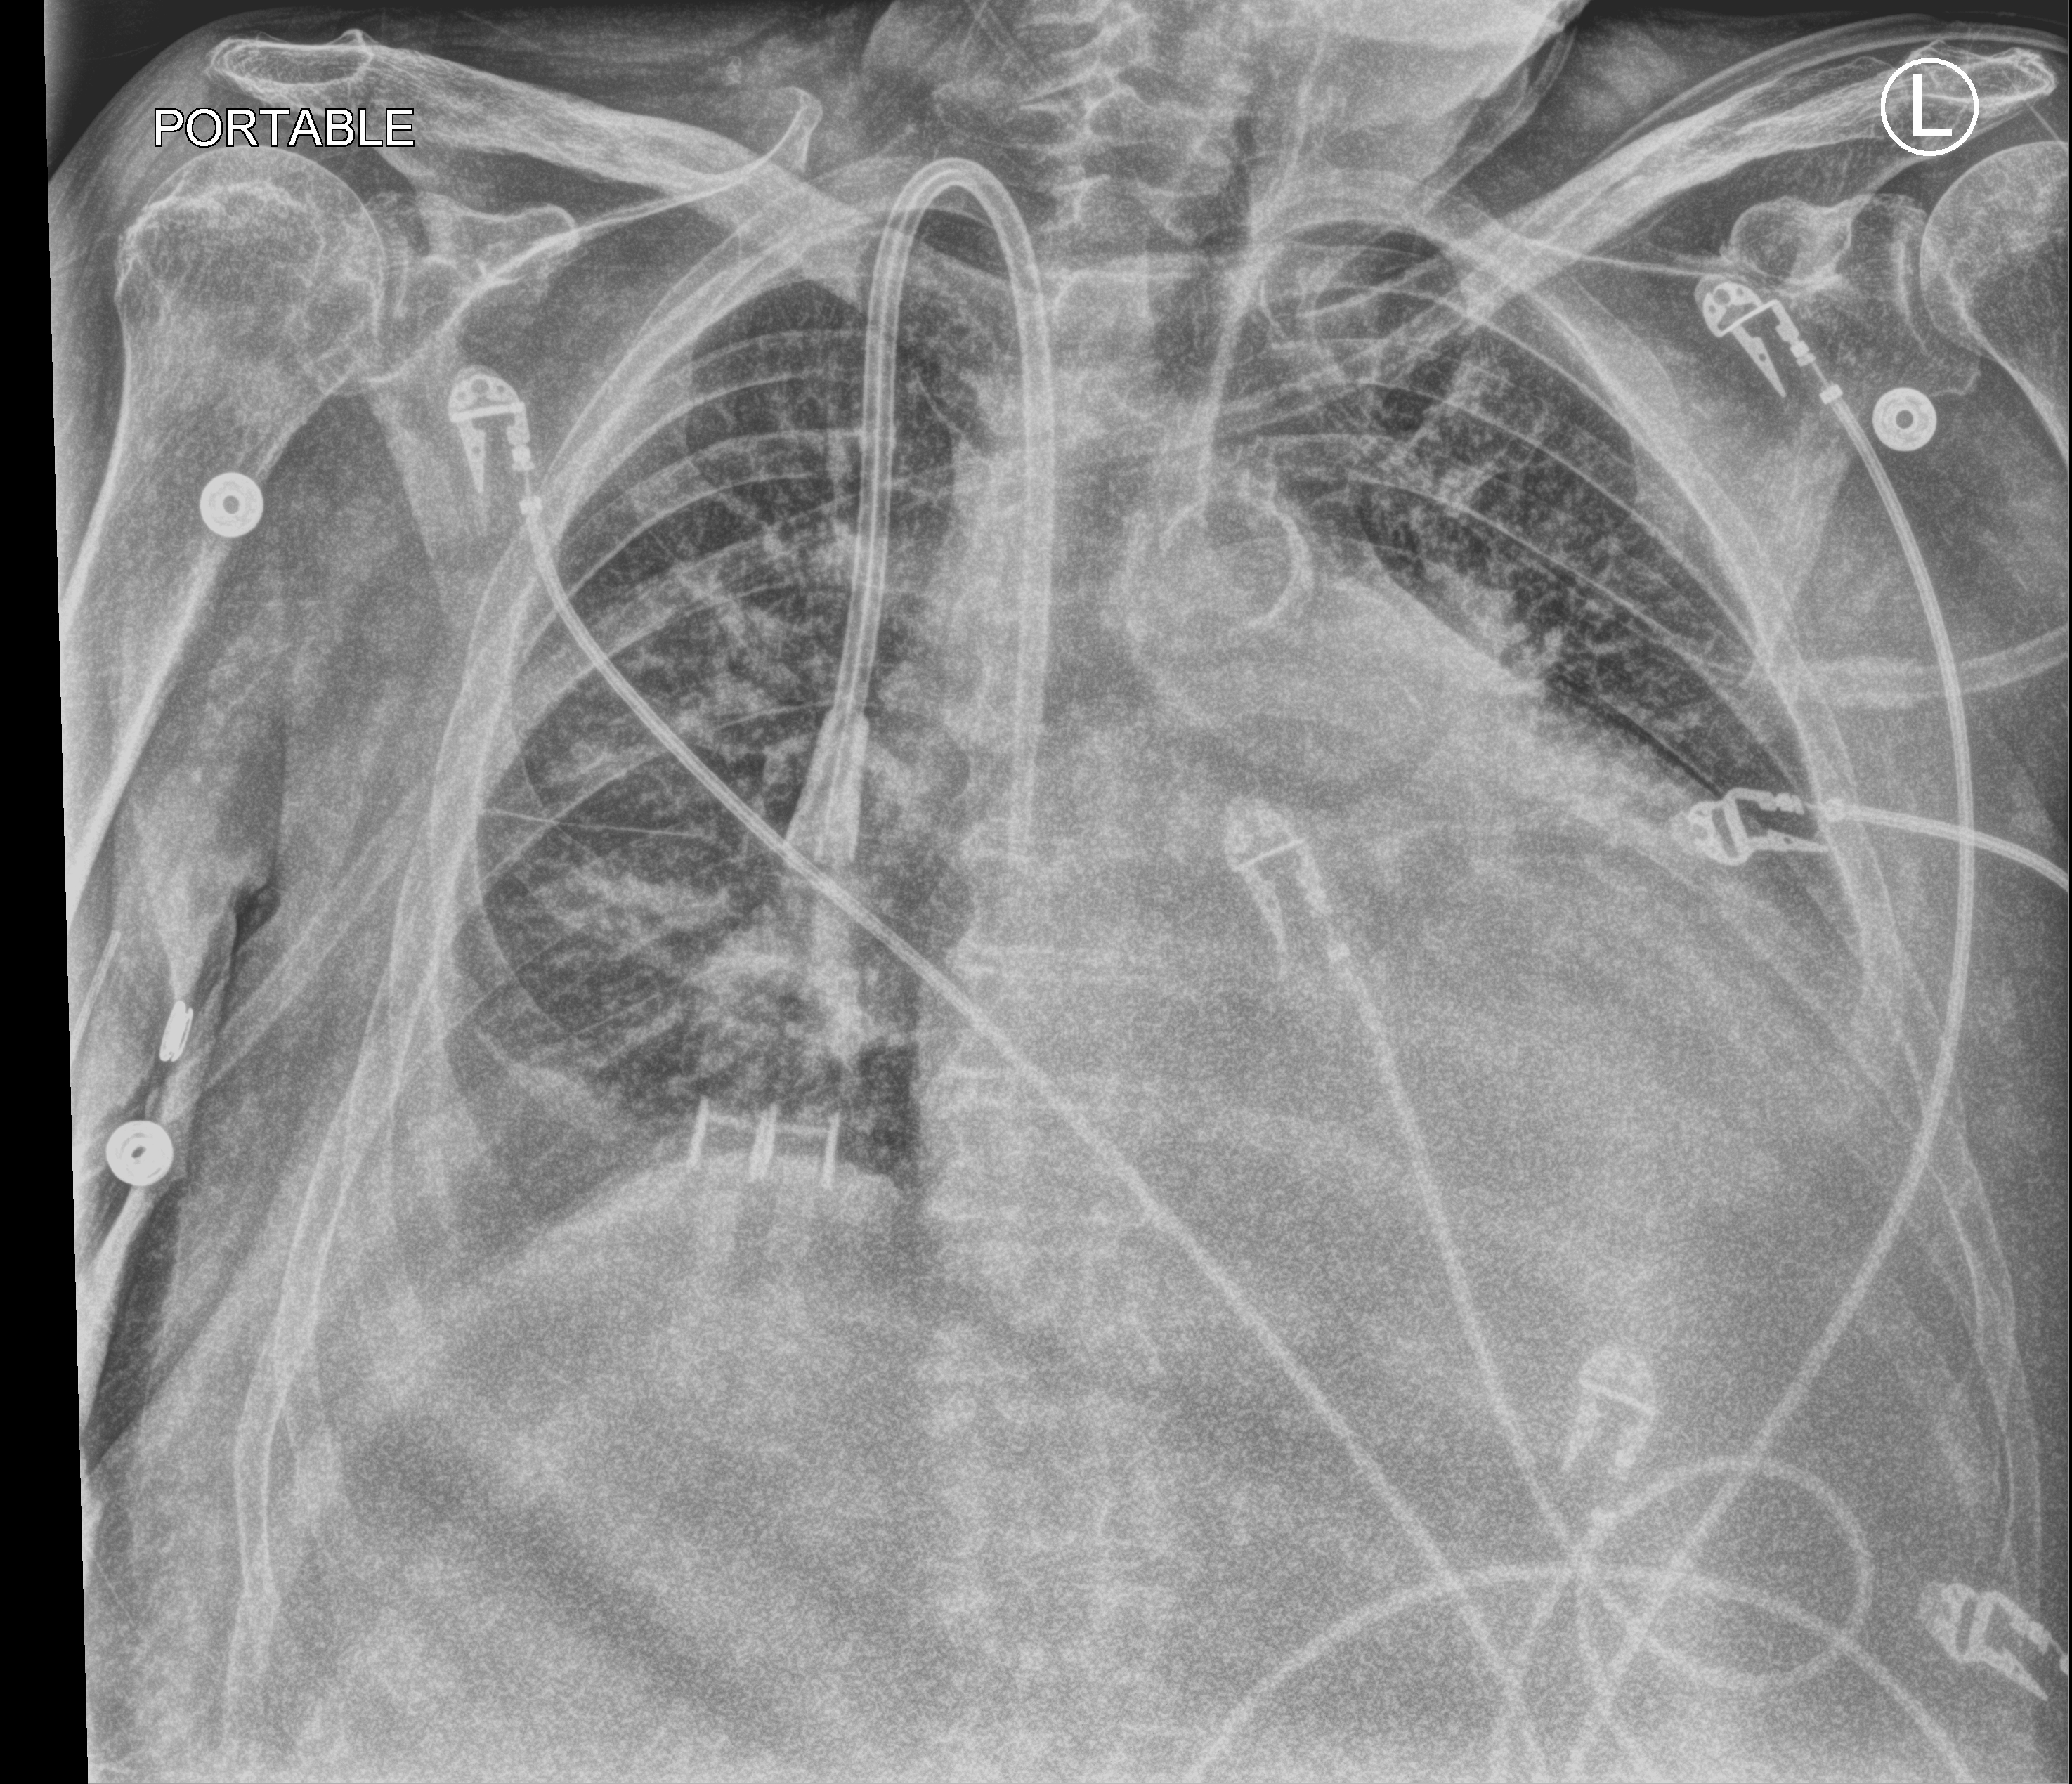
Chest X-ray (portable). Male patient hospitalised with COVID-19, age 60–74 years.
Hospital-stay facts (about this admission, not read from this image; timing relative to this image not recorded): admitted to intensive care during this hospital stay: yes; mechanically ventilated during this hospital stay: no; length of hospital stay: 4 days.